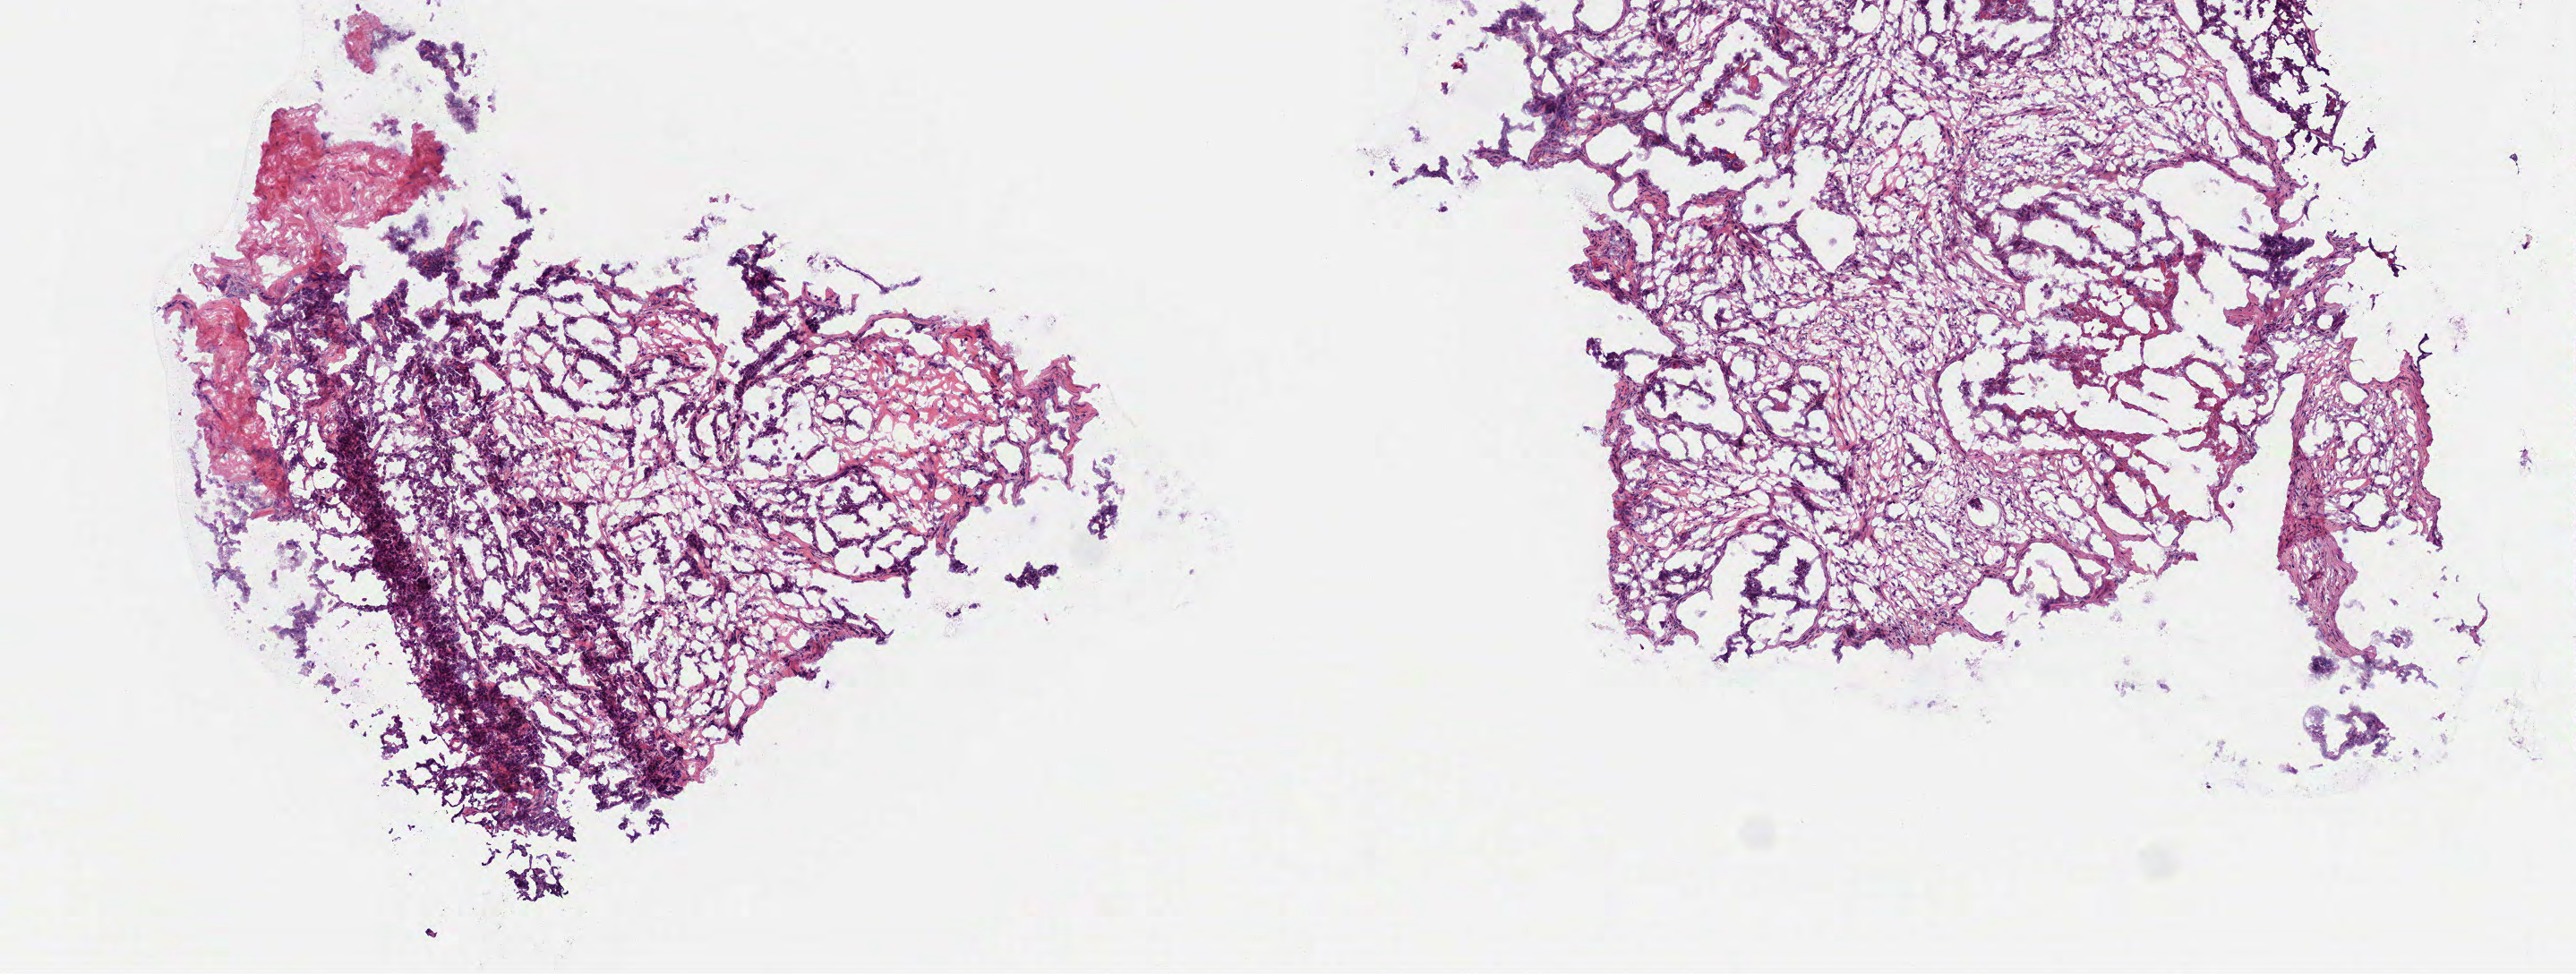
Whole-slide histology image, H&E, a low-resolution overview of the entire scanned area, about 5.8 x 2.2 mm. Frozen section from the bottom of the tissue portion. Sample: primary tumour, head and neck. Patient: male, age at initial diagnosis 55 years. Histologic grade: G3 (poorly differentiated). Slide review estimates, as recorded: tumour cells 60%, tumour nuclei 60%, normal cells 0%, stromal cells 40%, necrosis 0%.
Laterality: right. Diagnosis: Squamous cell carcinoma, NOS (overlapping lesion of lip, oral cavity and pharynx). AJCC pathologic stage: II (7th edition).